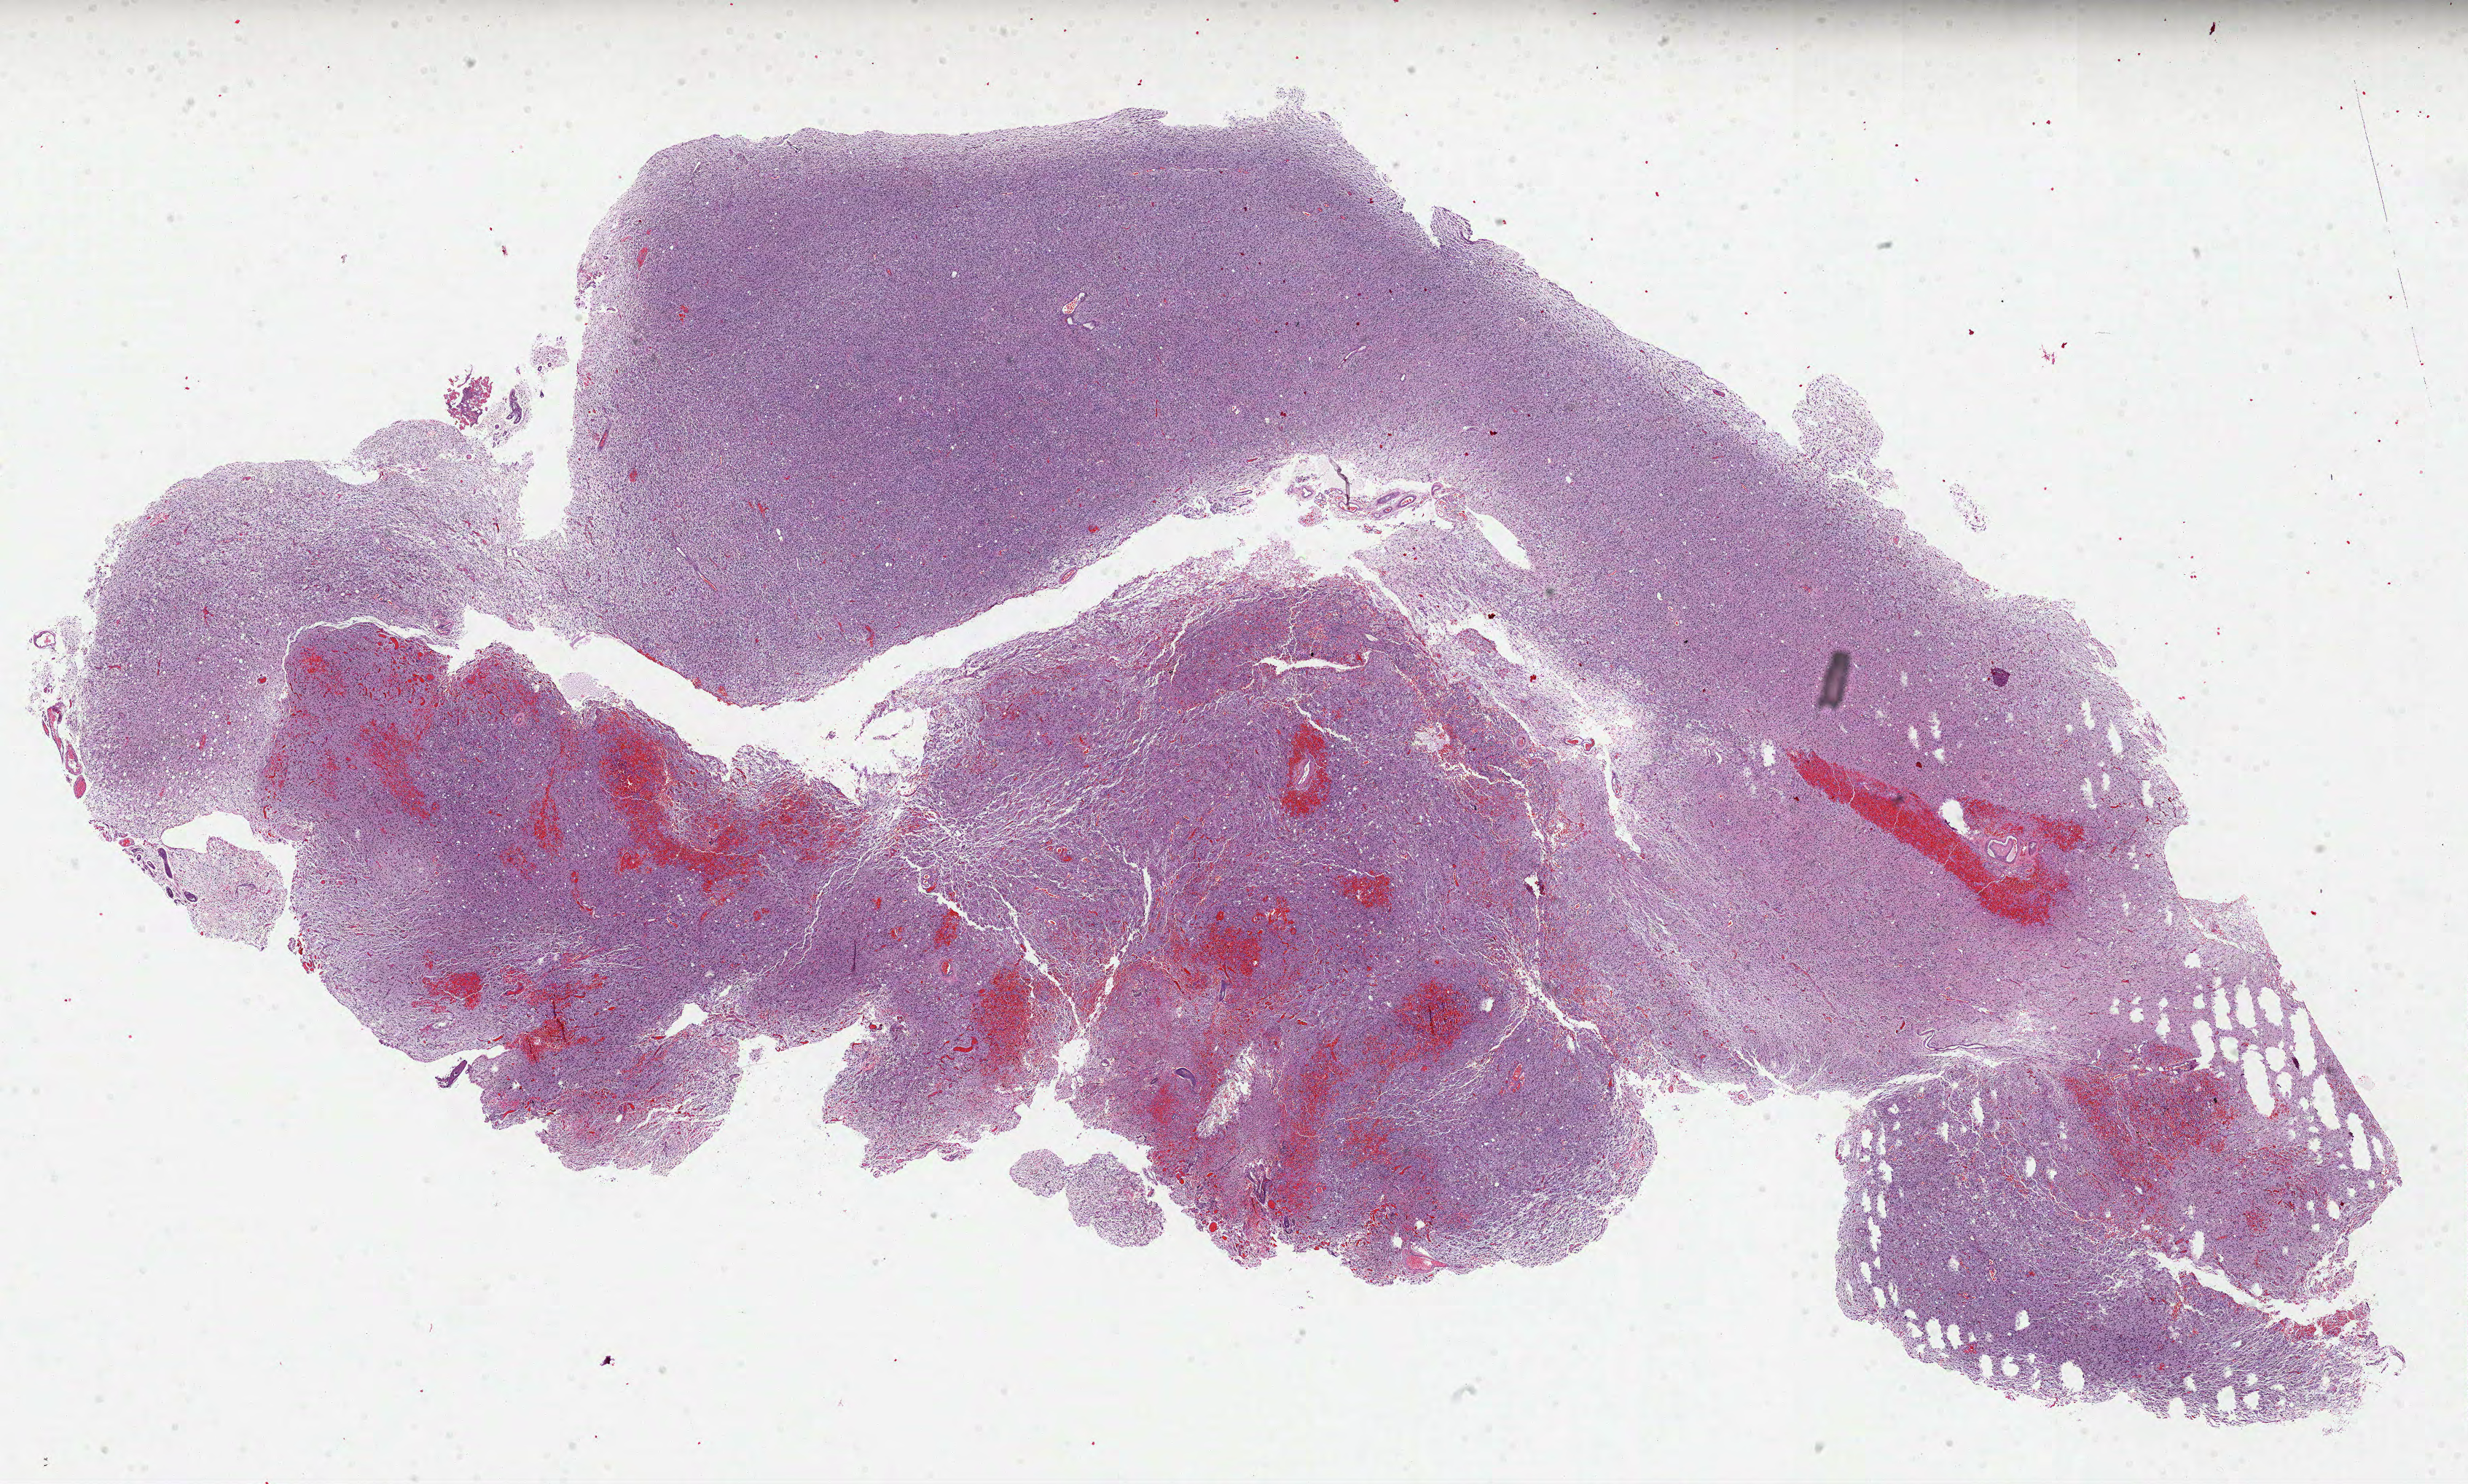
Hematoxylin and eosin (H&E) stained whole-slide image, shown as a low-resolution overview of the whole scanned area (about 27.3 x 16.4 mm, acquisition: 40x scan). Formalin-fixed paraffin-embedded (FFPE) diagnostic section. Sample: primary tumour, brain. Male patient; age at initial diagnosis 41 years. Histologic grade: G2 (moderately differentiated).
Histologic diagnosis: Astrocytoma, NOS (cerebrum).